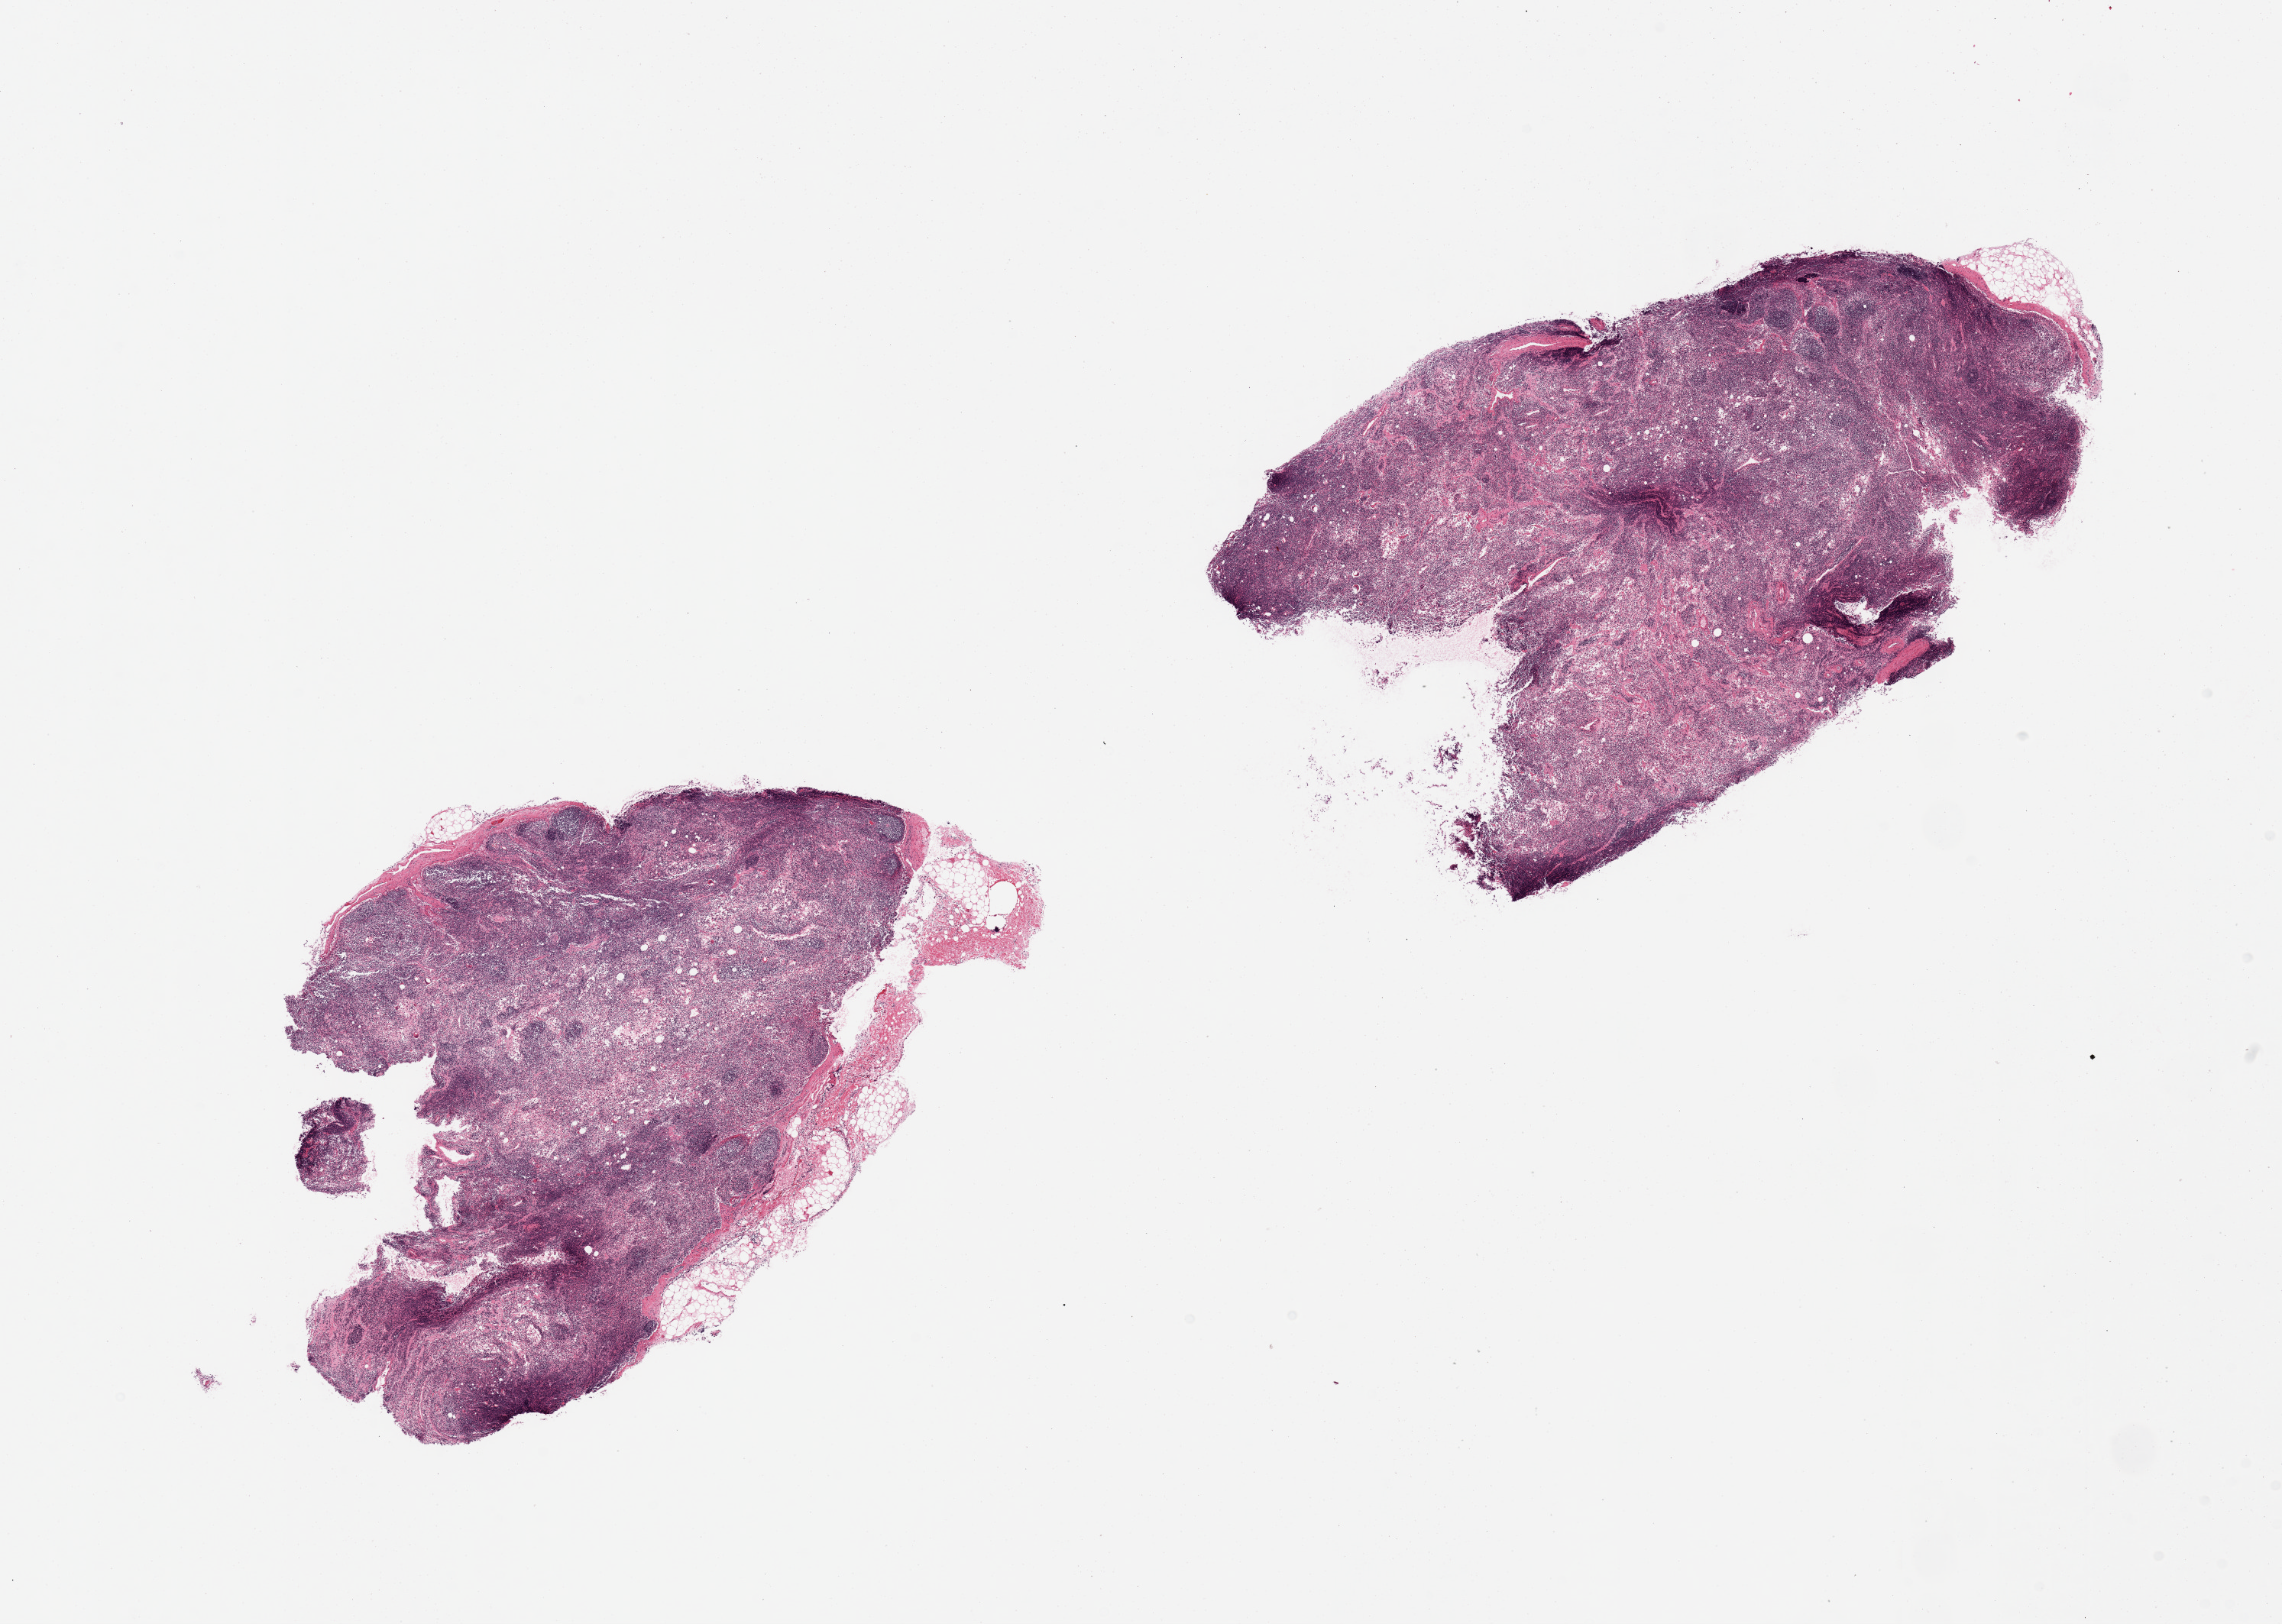
Whole-slide image, H&E stain — whole scanned area (about 23.6 x 16.8 mm, slide scanned at 20x) shown as a low-resolution overview. PAXgene-fixed, paraffin-embedded tissue. Section of pancreas (target tissue). Donor tissue sample. Donor sex: female.
• review note (as recorded): 2 pieces autolyzed lymph node, not pancreas